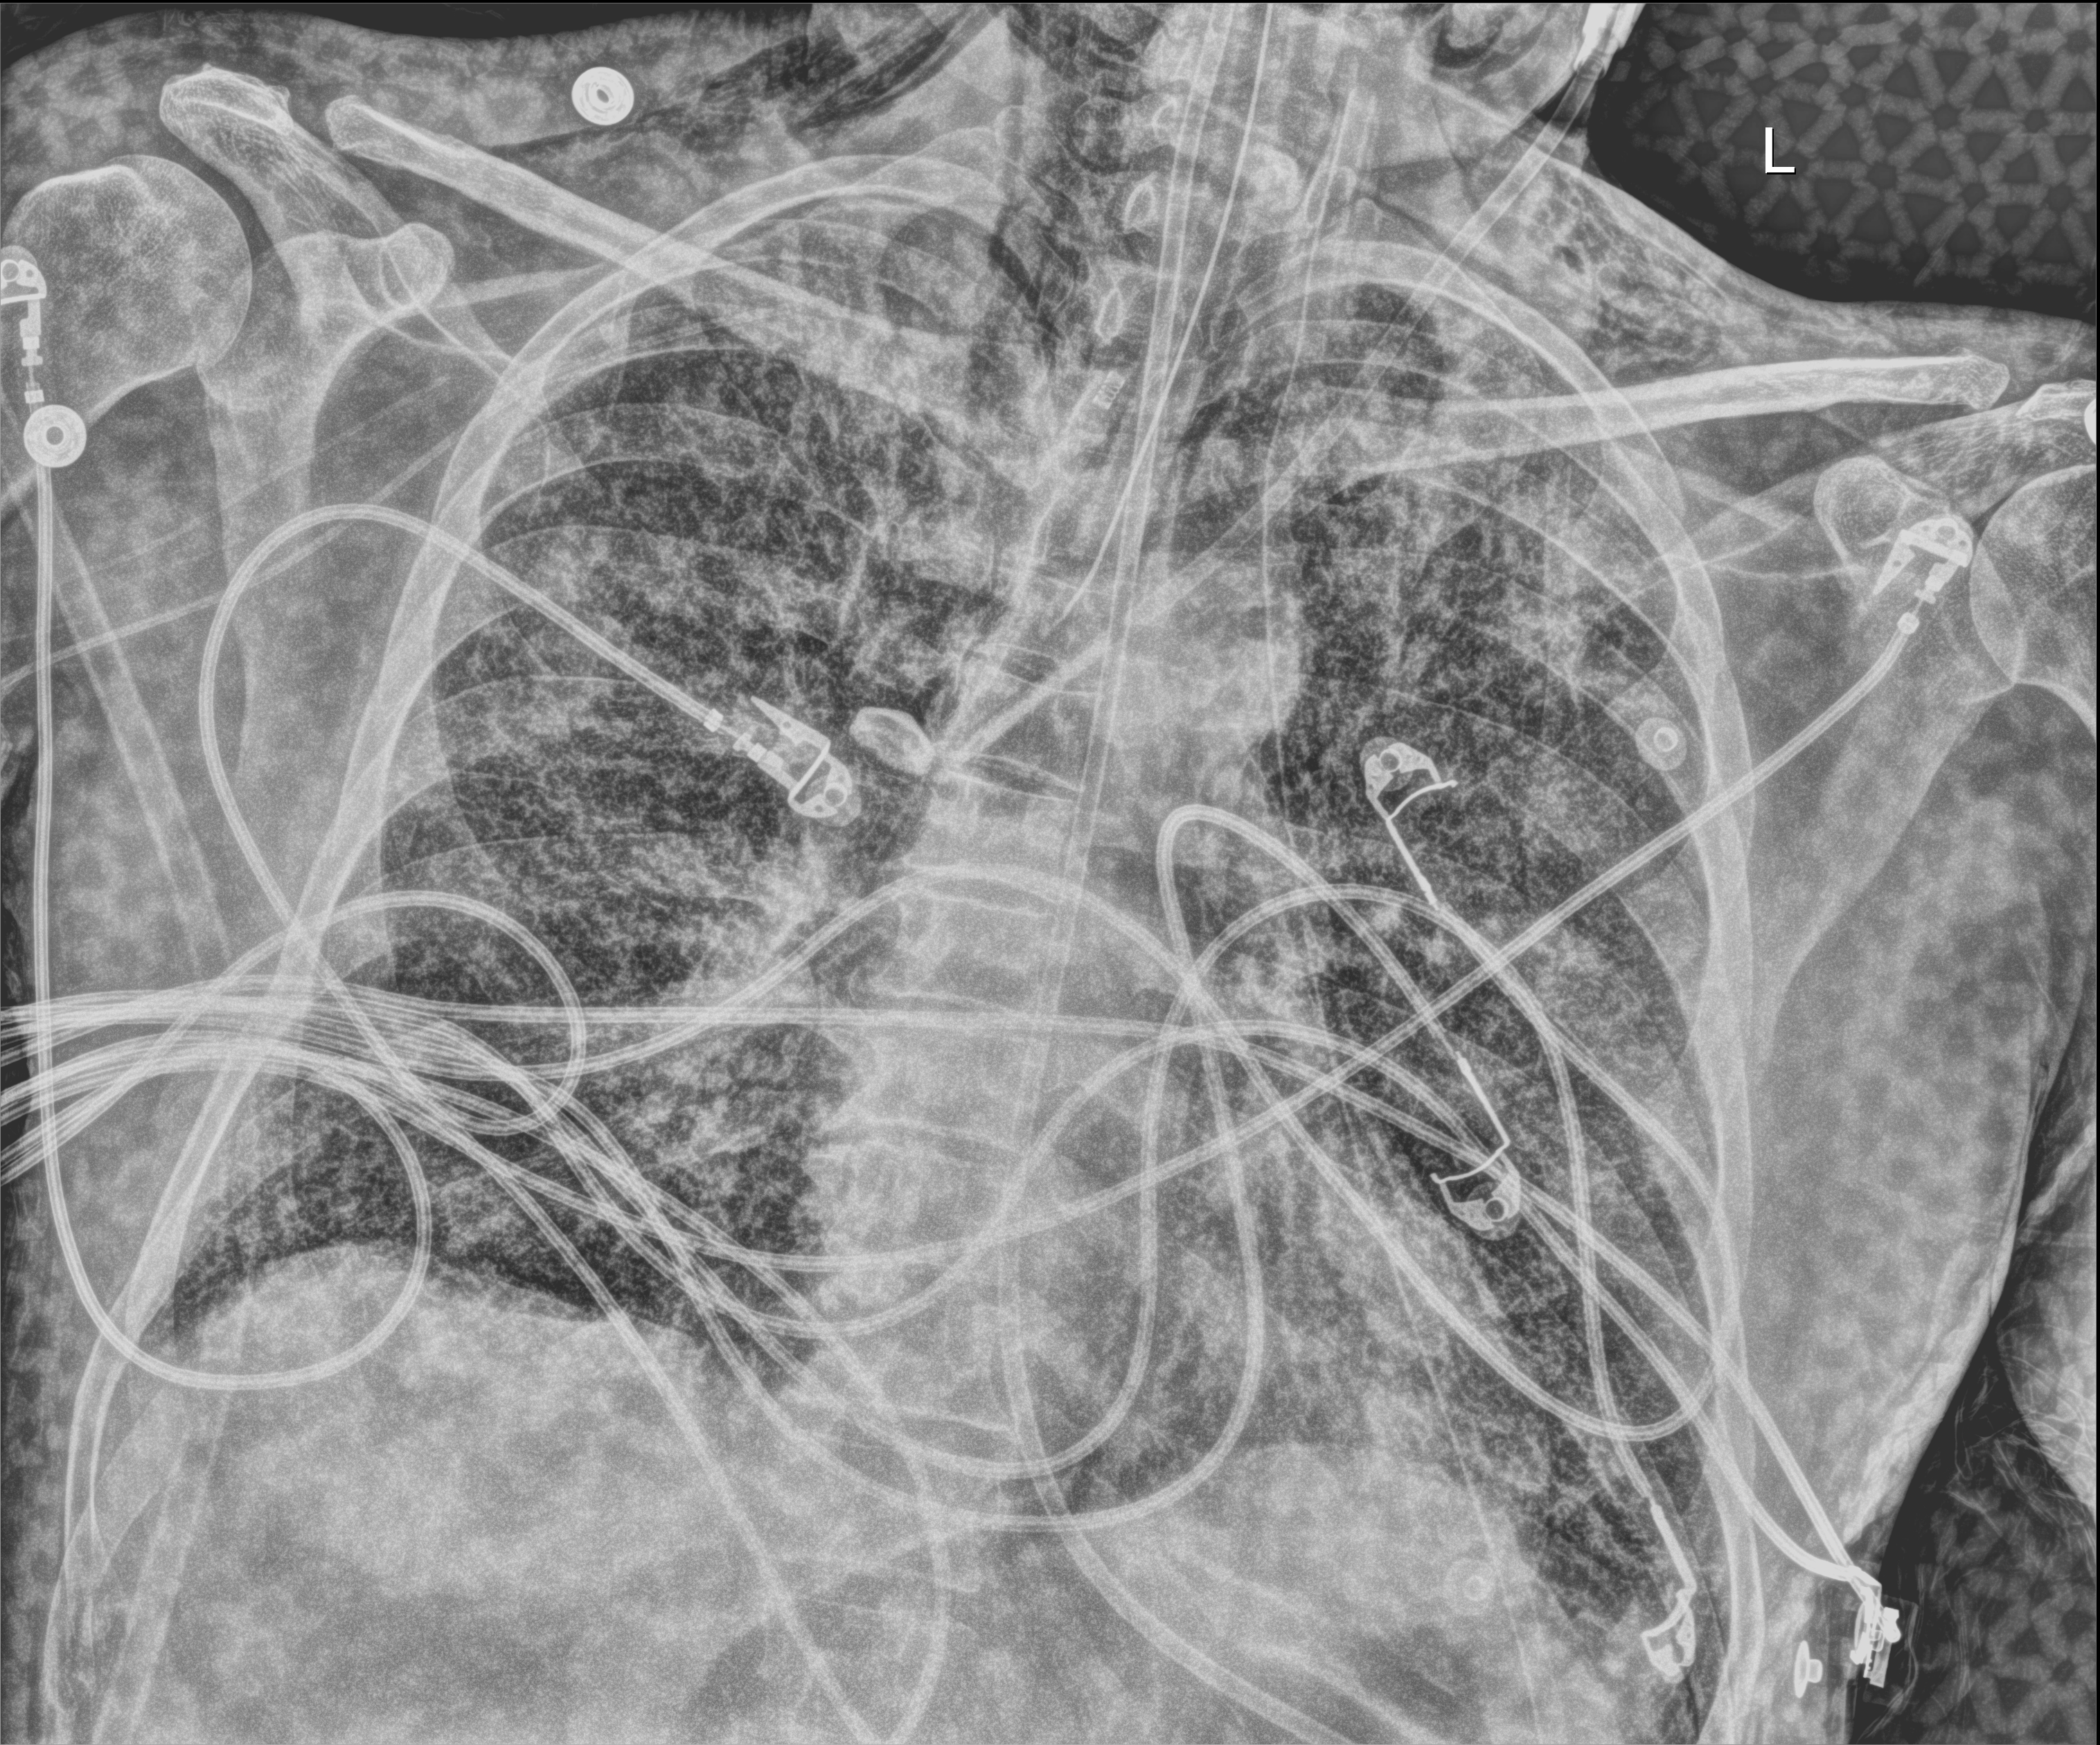
Chest X-ray (portable), anteroposterior (AP) projection. Male patient hospitalised with COVID-19, age 18–59 years.
Hospital-stay facts (about this admission, not read from this image; timing relative to this image not recorded):
- mechanically ventilated during this hospital stay: yes